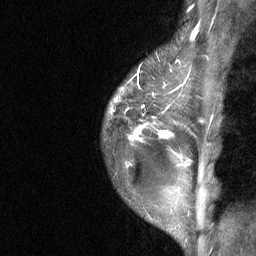
Breast MRI (dynamic contrast-enhanced), one sagittal slice. Position 52 of 64 along the scan axis. Dynamic contrast-enhanced study with each time point stored as its own series, time point 2 of 3 at this slice position (early post-contrast, ordered by acquisition time). 1.5 T. TE 4.8 ms, TR 27 ms. 256 × 256 image matrix, field of view 180 × 180 mm. Patient: female, 34 years. Case-level facts recorded for this patient, not image findings: setting: breast cancer imaged before/during neoadjuvant chemotherapy; receptor status: HR-positive, HER2-negative.
Annotated regions visible in this slice (semi-automatically segmented with operator editing):
- analysis volume of interest (the breast-tissue region the enhancement analysis was run in; not a lesion): box from (x=102, y=44) to (x=181, y=191) px
- tumour enhancement mask (voxels above the 90 % enhancement threshold inside the analysis volume of interest): (x=129, y=105)–(x=172, y=139)